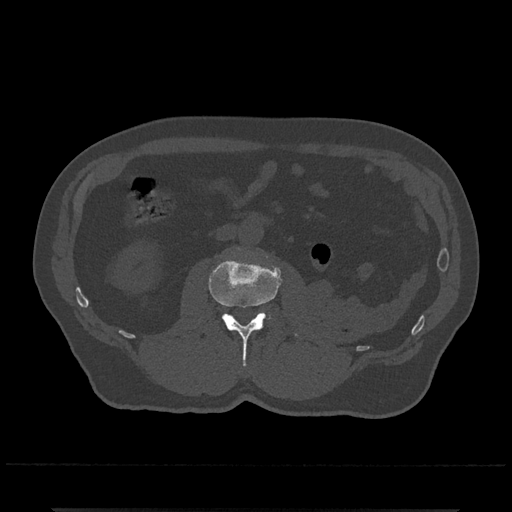
CT including the spine, one axial slice; position 281 of 797 along the scan axis; reconstruction kernel Br40s/3; 120 kVp; bone window (W 1800 / L 400 HU); 0.5 mm slice thickness; 512 × 512 image matrix. Male patient, age 67 years. From the clinical record (not read from this slice): primary cancer: prostate.
Outlined on this slice (semi-automatic segmentation, software-assisted and operator-edited):
- L2 vertebra: bounding box <208,247,298,367> (left, top, right, bottom; pixels)
- L3 vertebra: <258,312,268,317>